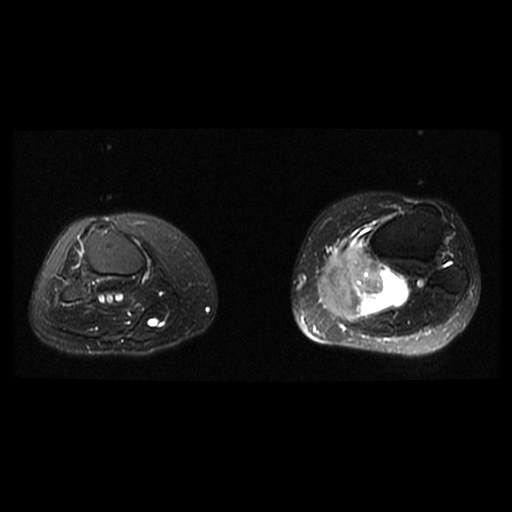
MRI of an extremity soft-tissue mass, one axial slice. Position 22 of 38 along the scan axis. T2-weighted fat-saturated. 6 mm slice thickness. 512 × 512 image matrix, field of view 330 × 330 mm. Female patient. Case-level facts recorded for this patient, not image findings: histological type: extraskeletal high grade osteogenic sarcoma; grade: high; site of the primary tumour: left calf.
Annotated regions visible in this slice (manually delineated by an expert):
- gross tumour volume (mass): box from (x=318, y=242) to (x=410, y=321) px